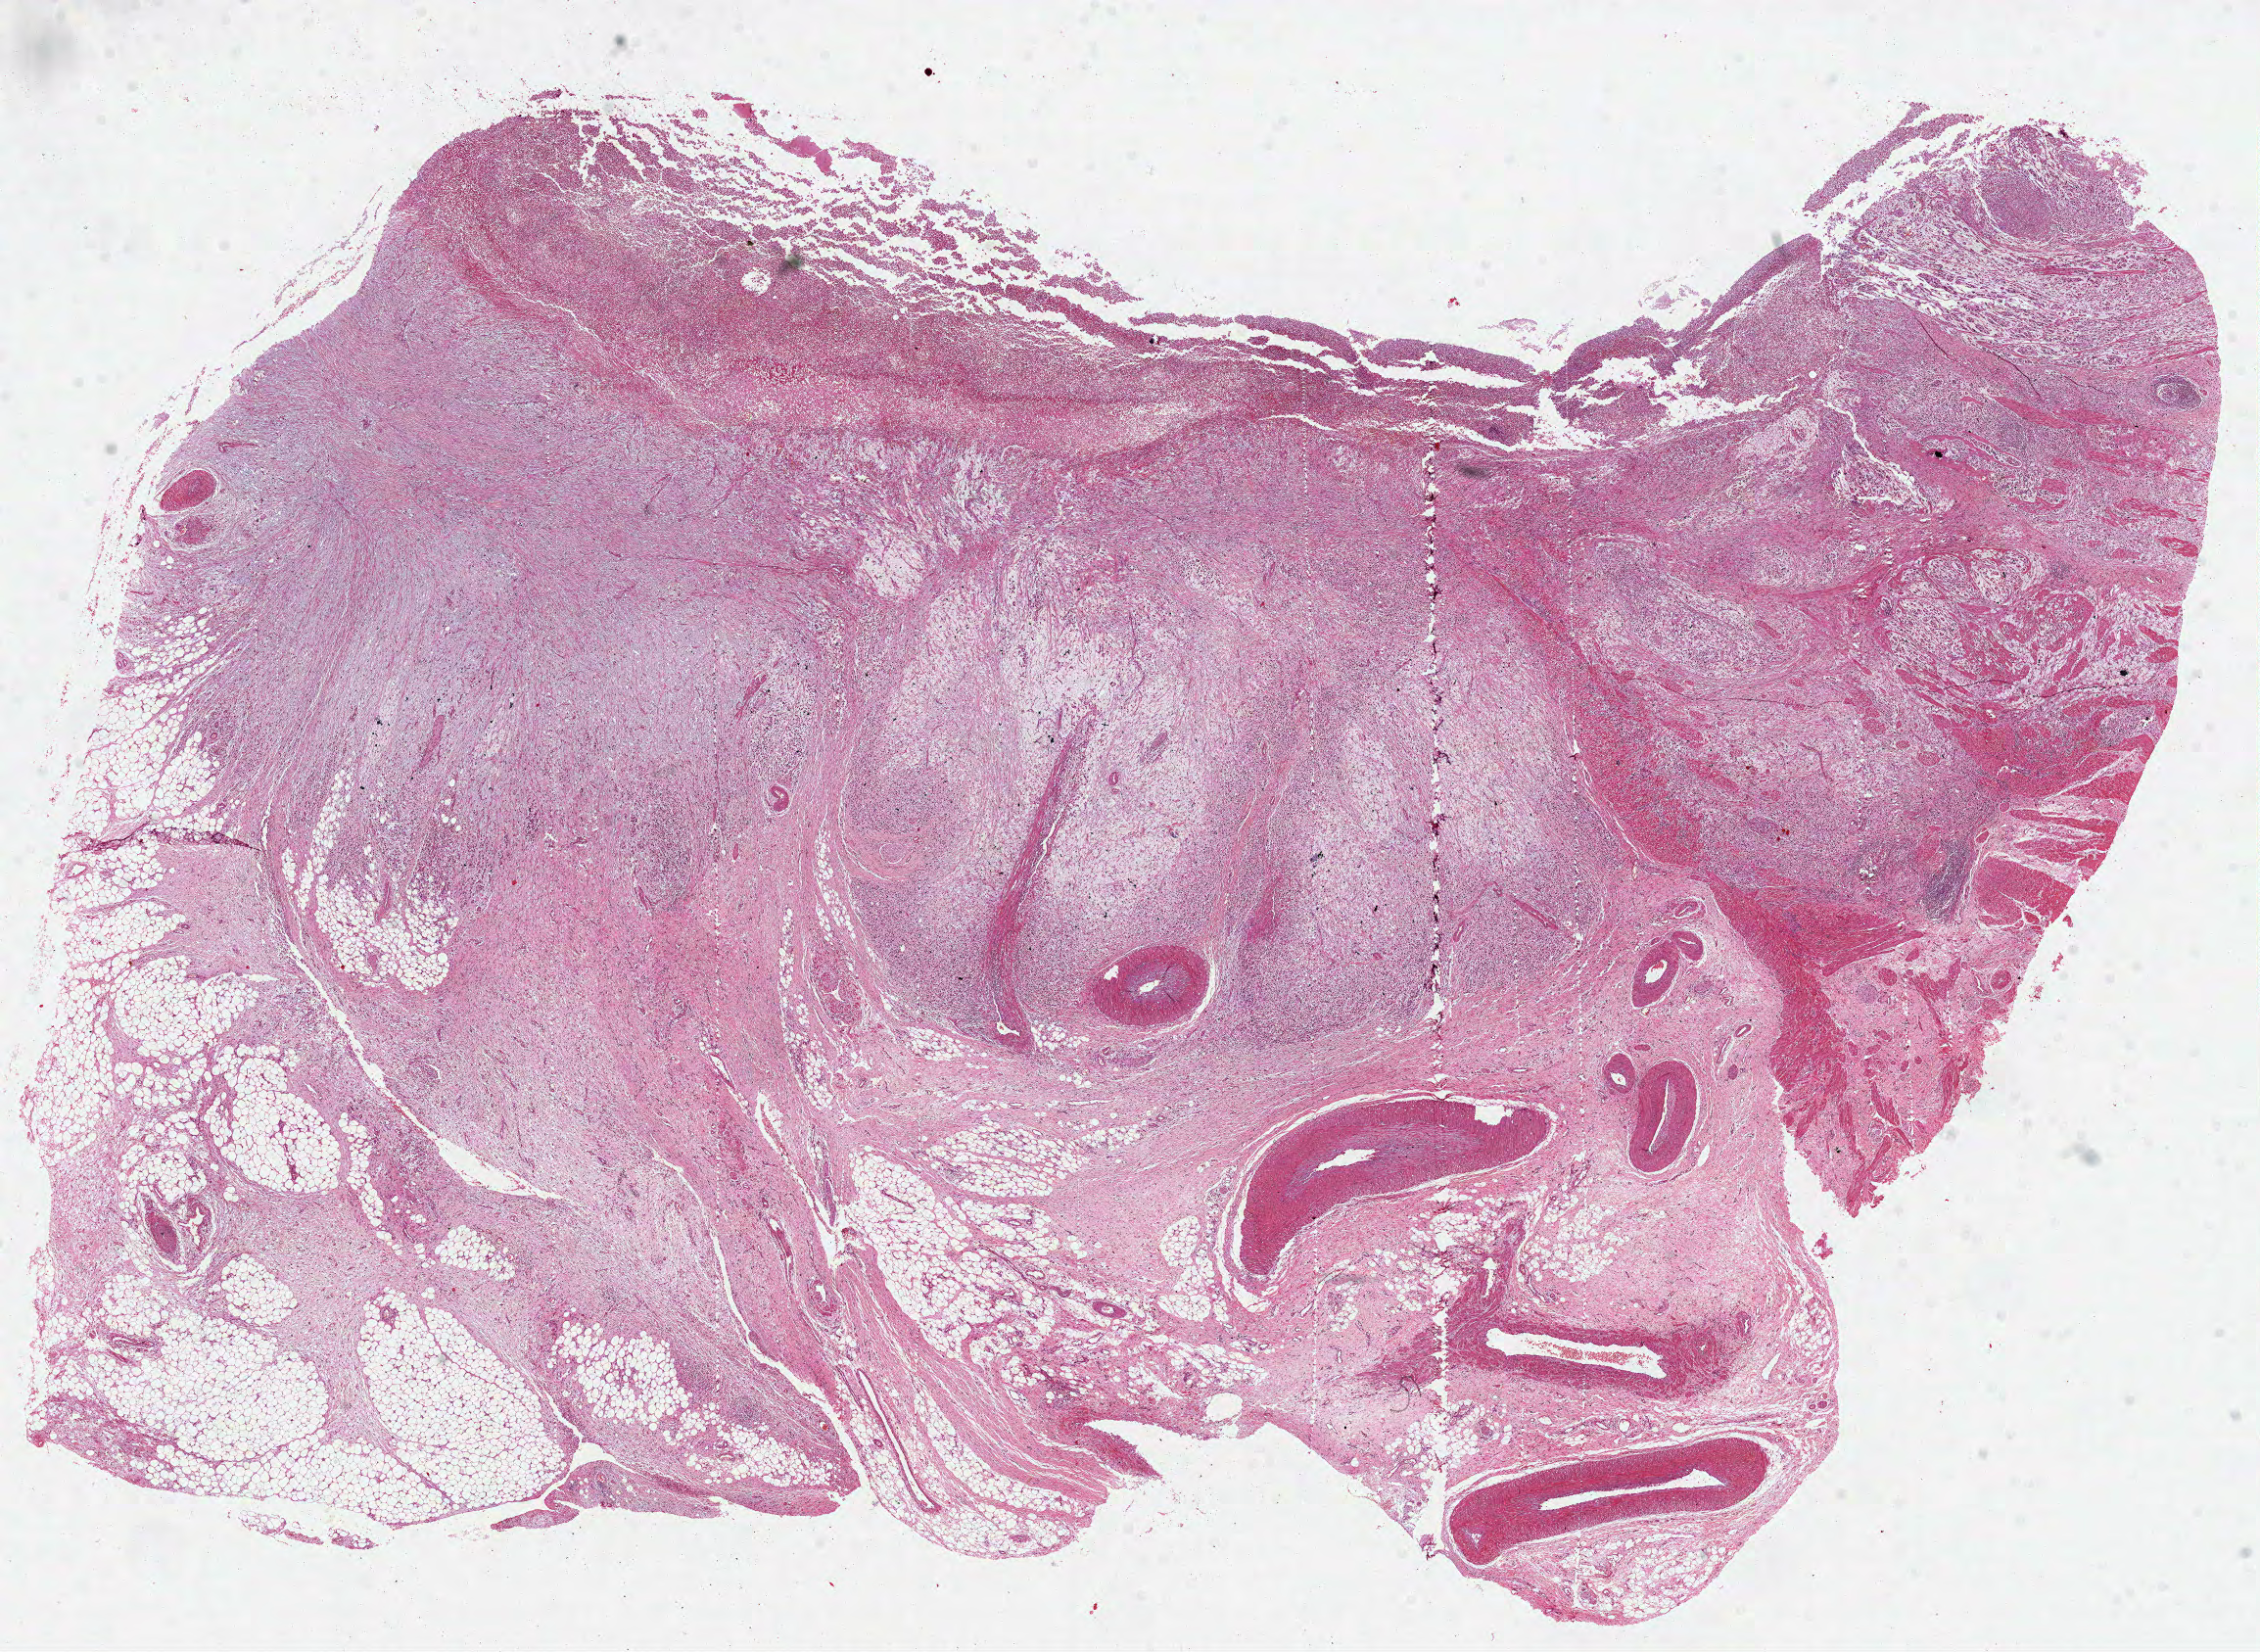
Digitized Hematoxylin and eosin (H&E) stained tissue section (whole slide), shown as a low-resolution overview of the whole scanned area (about 18.6 x 13.6 mm, slide scanned at 40x). Formalin-fixed paraffin-embedded (FFPE) diagnostic section. Primary tumour sample from the stomach. Patient: male, age at initial diagnosis 60 years. Histologic grade: G3 (poorly differentiated).
AJCC pathologic stage: II (6th edition). Diagnosis: Mucinous adenocarcinoma (body of stomach).